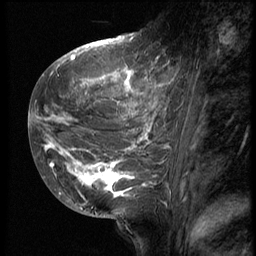
Breast MRI (dynamic contrast-enhanced), one sagittal slice; position 22 of 62 along the scan axis; 3 images stored at this slice position (order not interpretable as contrast timing); 1.5 T; TE 4.2 ms, TR 9 ms; 2.5 mm slice thickness; 256 × 256 image matrix, field of view 180 × 180 mm. Patient: female, 28 years. From the clinical record (not read from this slice): setting: breast cancer imaged before/during neoadjuvant chemotherapy.
Structures marked on this image (semi-automatic segmentation, software-assisted and operator-edited):
- analysis volume of interest (the breast-tissue region the enhancement analysis was run in; not a lesion): bounding box (x1, y1, x2, y2) in pixels: (42, 45, 176, 207)
- tumour enhancement mask (voxels above the 140 % enhancement threshold inside the analysis volume of interest): (42, 54, 166, 202)